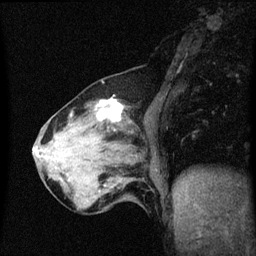
Breast MRI (dynamic contrast-enhanced), one sagittal slice; position 21 of 60 along the scan axis; dynamic contrast-enhanced series, image 2 of 3 at this slice position (ordered by acquisition); 1.5 T; TE 4.2 ms, TR 8.4 ms; 2 mm slice thickness; 256 × 256 image matrix, field of view 200 × 200 mm. Patient: female, 64 years. From the clinical record (not read from this slice): setting: breast cancer imaged before/during neoadjuvant chemotherapy; receptor status: HR-positive, HER2-negative.
Outlined on this slice (semi-automatically segmented with operator editing):
- analysis volume of interest (the breast-tissue region the enhancement analysis was run in; not a lesion): bounding box [x1, y1, x2, y2] px = [56, 96, 138, 175]
- tumour enhancement mask (voxels above the 70 % enhancement threshold inside the analysis volume of interest): [99, 100, 124, 121]